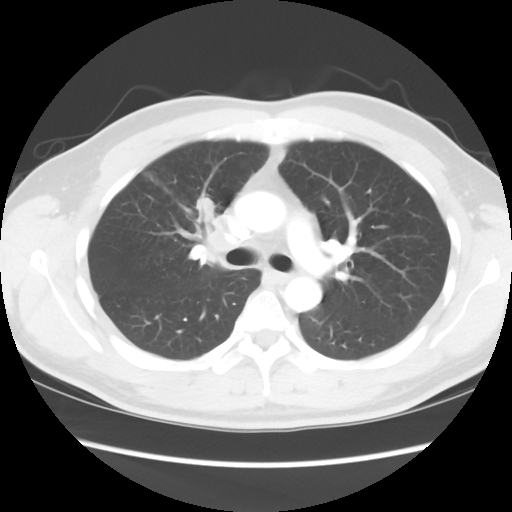
Chest CT, one axial slice. Slice 60 of 80 in the series (ordered by position). 120 kVp. Lung window (W 1500 / L -600 HU). 512 × 512 image matrix, field of view 360 × 360 mm. Patient: male, 35 years. From the clinical record (not read from this slice): clinical TNM (as recorded): T1c N1 M1b.
Outlined on this slice (rectangle marked by the reading radiologist):
- lung tumour (recorded histology: adenocarcinoma): bounding box [x1, y1, x2, y2] px = [195, 194, 236, 262]